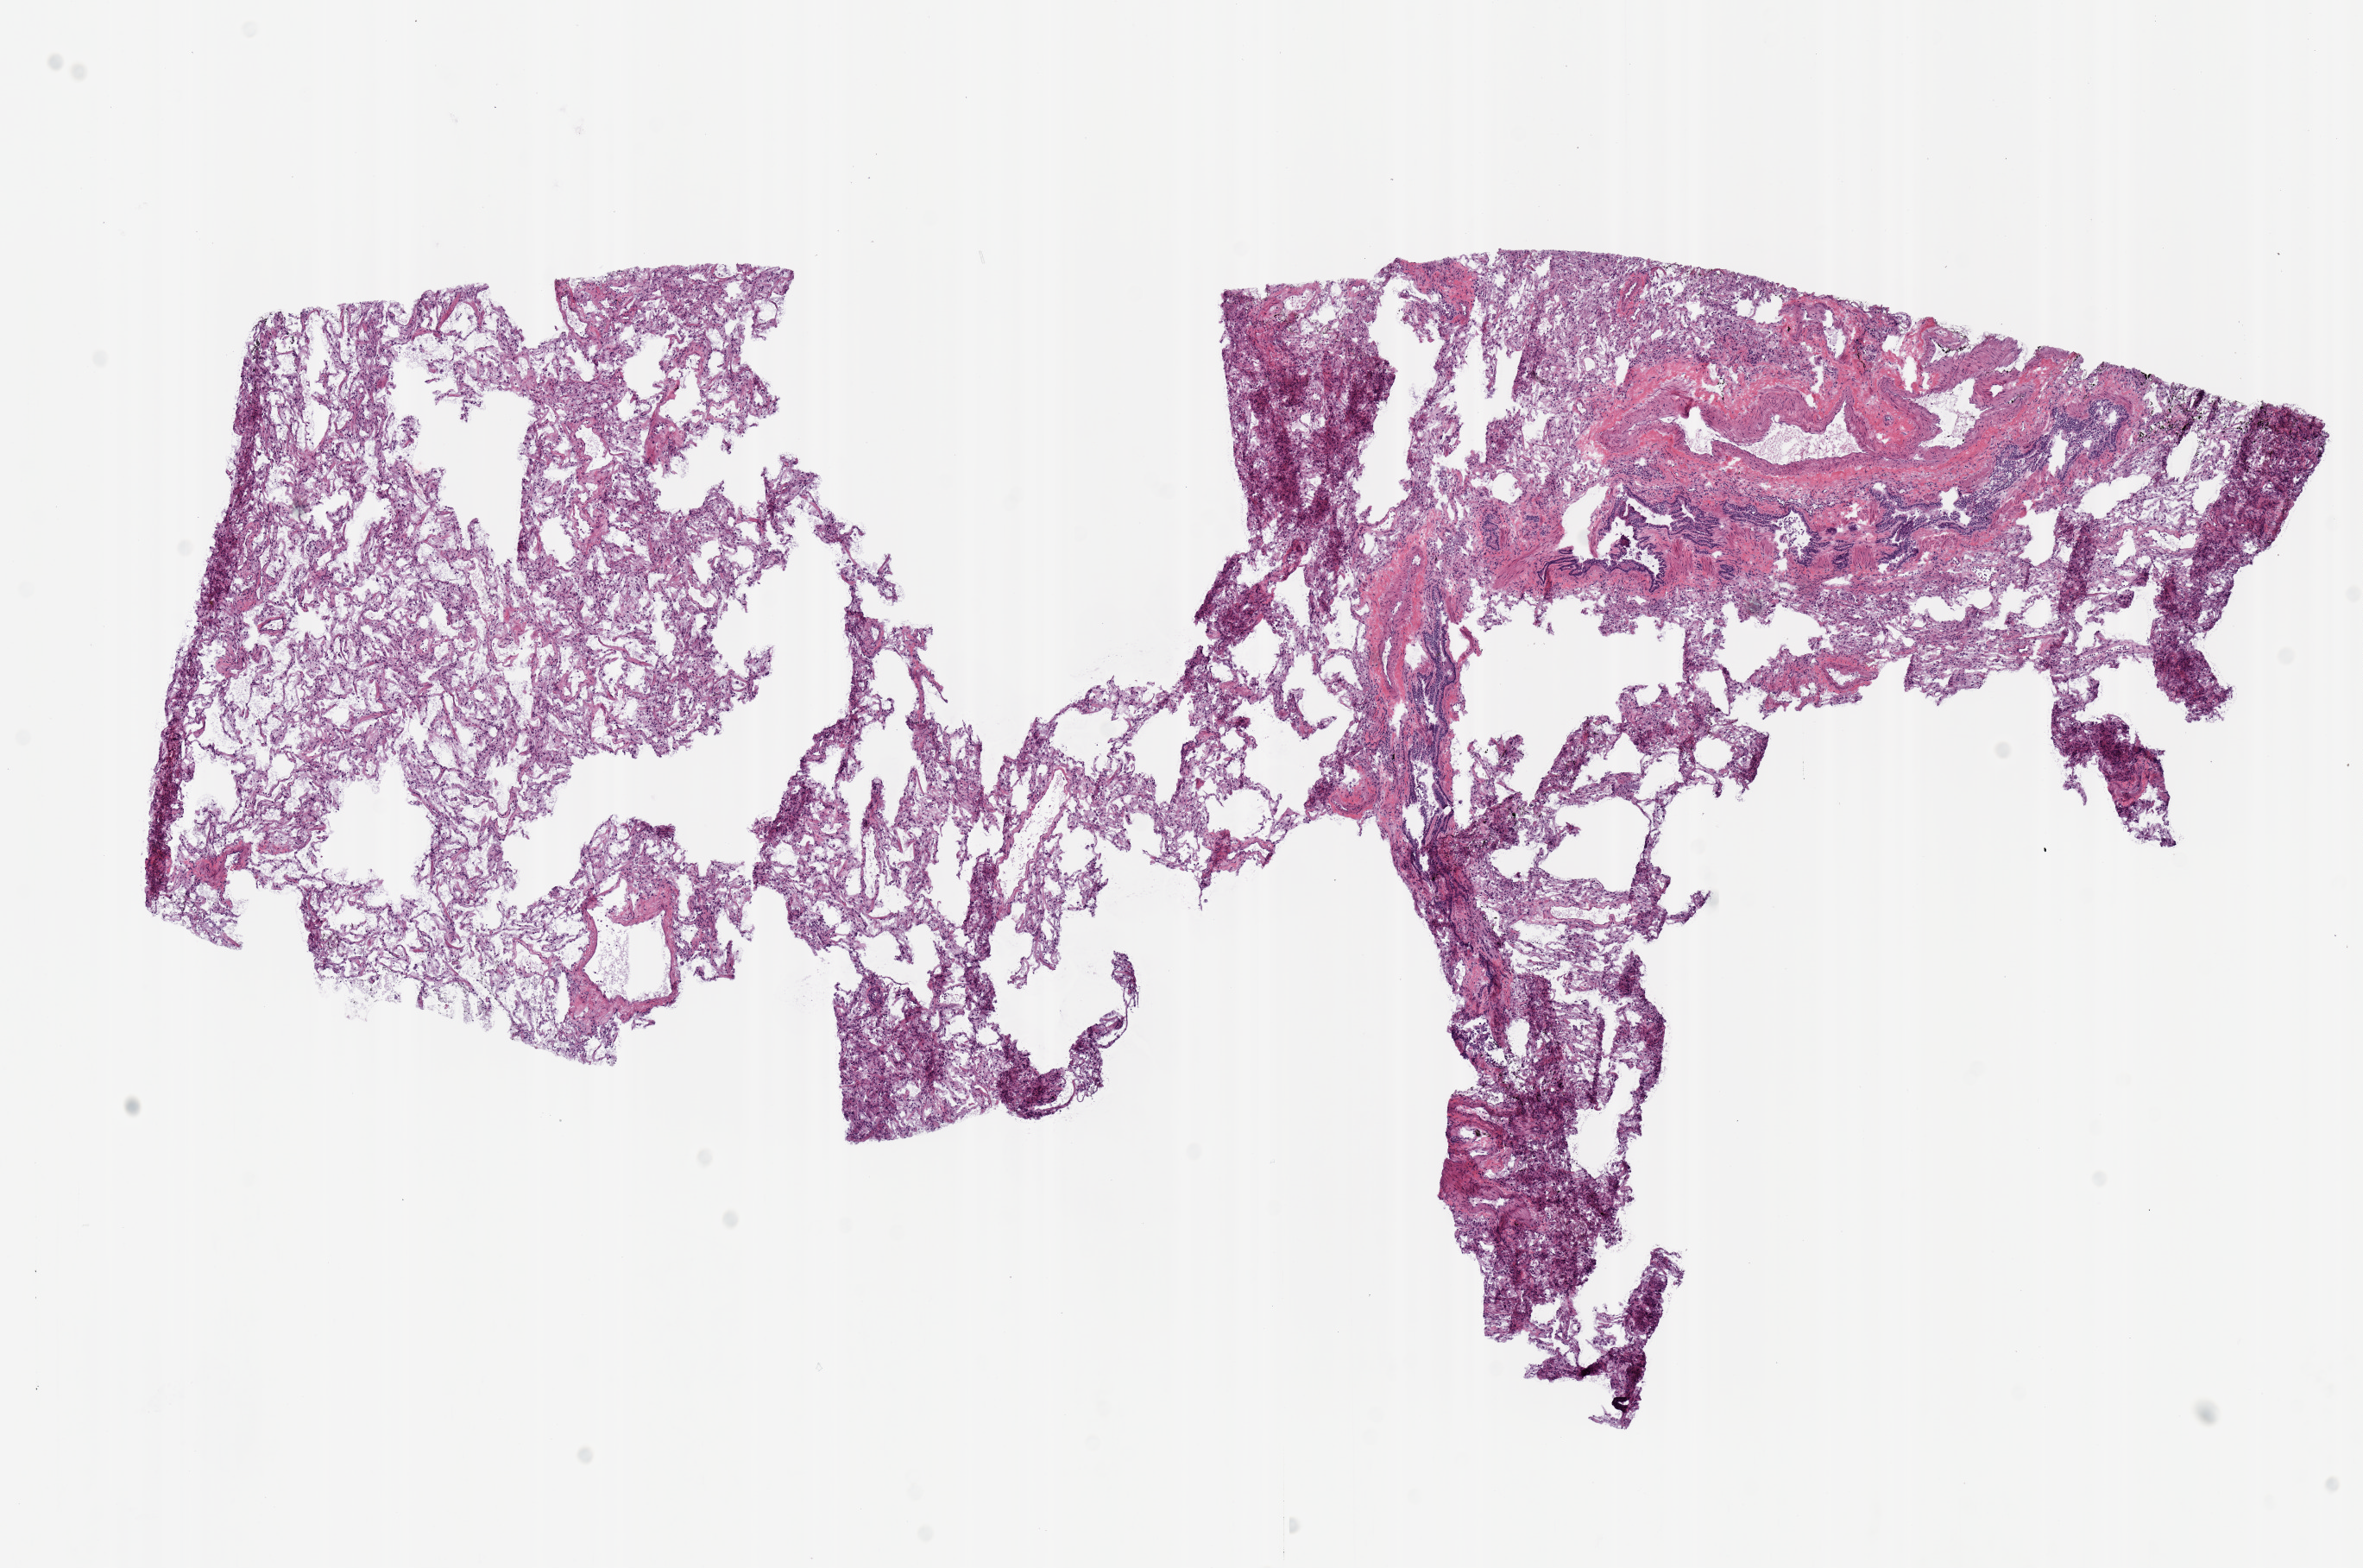
Digitized H&E tissue section (whole slide) — whole scanned area (about 10.8 x 7.2 mm, slide scanned at 20x) shown as a low-resolution overview, frozen section from the top of the tissue portion, lung, solid tissue normal (non-tumour tissue) sample. Patient: female, age at initial diagnosis 74 years.
• this section: solid tissue normal sample (biorepository sample class)
• patient diagnosis: Bronchiolo-alveolar carcinoma, non-mucinous (lower lobe, lung)